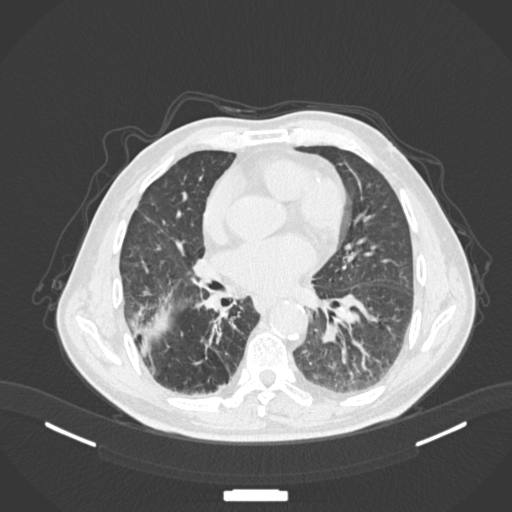
Chest CT, one axial slice. Position 71 of 201 along the scan axis. Reconstruction kernel B30f. Lung window (W 1500 / L -600 HU). 1 mm slice thickness. 512 × 512 image matrix, field of view 400 × 400 mm. Patient: male, 72 years. From the clinical record (not read from this slice): clinical TNM (as recorded): T3 N2 M0.
Outlined on this slice (rectangle marked by the reading radiologist):
- lung tumour (recorded histology: adenocarcinoma): bounding box <134,306,172,354> (left, top, right, bottom; pixels)